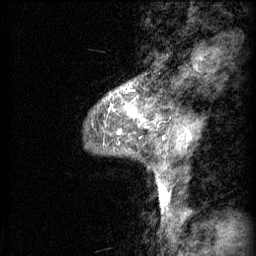
Breast MRI (dynamic contrast-enhanced), one sagittal slice. Slice 16 of 60 in the series (ordered by position). 3 images stored at this slice position (order not interpretable as contrast timing). 1.5 T. TE 4.2 ms, TR 11 ms. 2 mm slice thickness. 256 × 256 image matrix, field of view 200 × 200 mm. Patient: female, 48 years.
Annotated regions visible in this slice (semi-automatic segmentation, software-assisted and operator-edited):
- analysis volume of interest (the breast-tissue region the enhancement analysis was run in; not a lesion): bounding box <106,84,142,131> (left, top, right, bottom; pixels)
- tumour enhancement mask (voxels above the 70 % enhancement threshold inside the analysis volume of interest): <112,104,136,131>